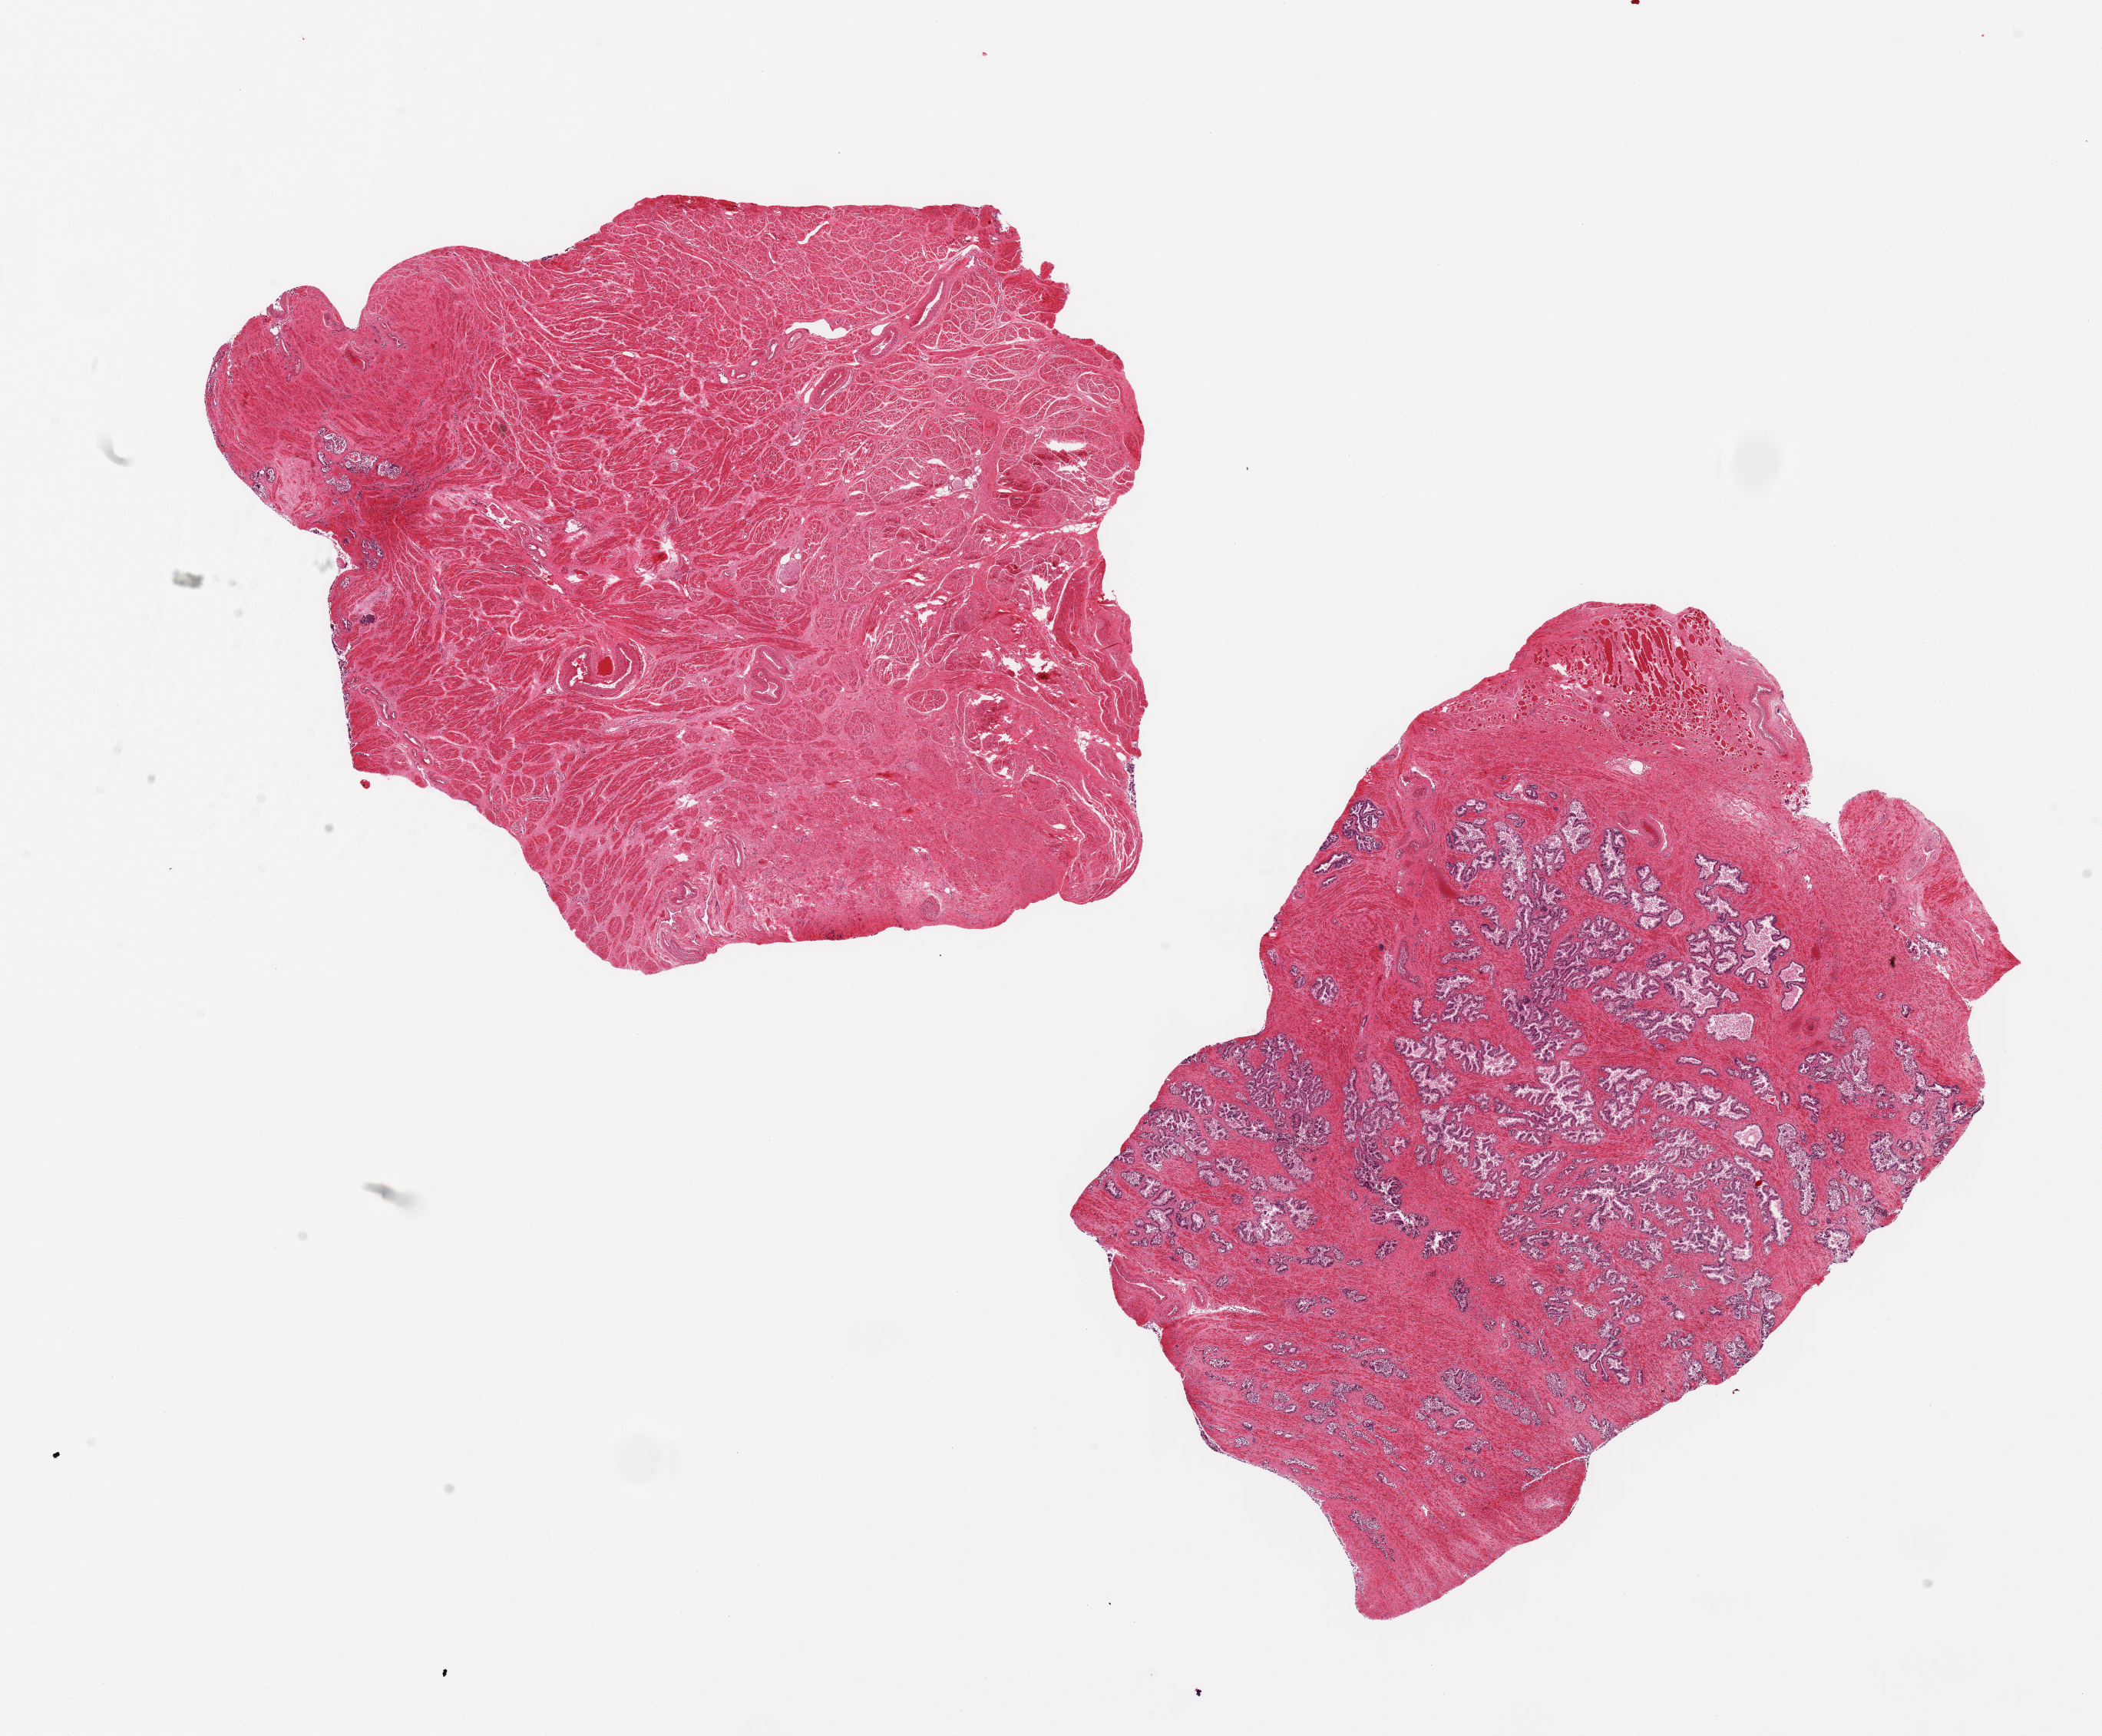
Hematoxylin and eosin (H&E) whole-slide image — low-resolution overview of the scanned area, about 21.7 x 17.9 mm; PAXgene-fixed paraffin-embedded (PFPE) section; section of prostate (target tissue); donor tissue sample. Donor sex: male.
Reviewer comment on this tissue sample: 2 ~9.5x7.5mm aliquots, one with prominent glandular hyperplasia; the other with prominent stromal hyperplasia.